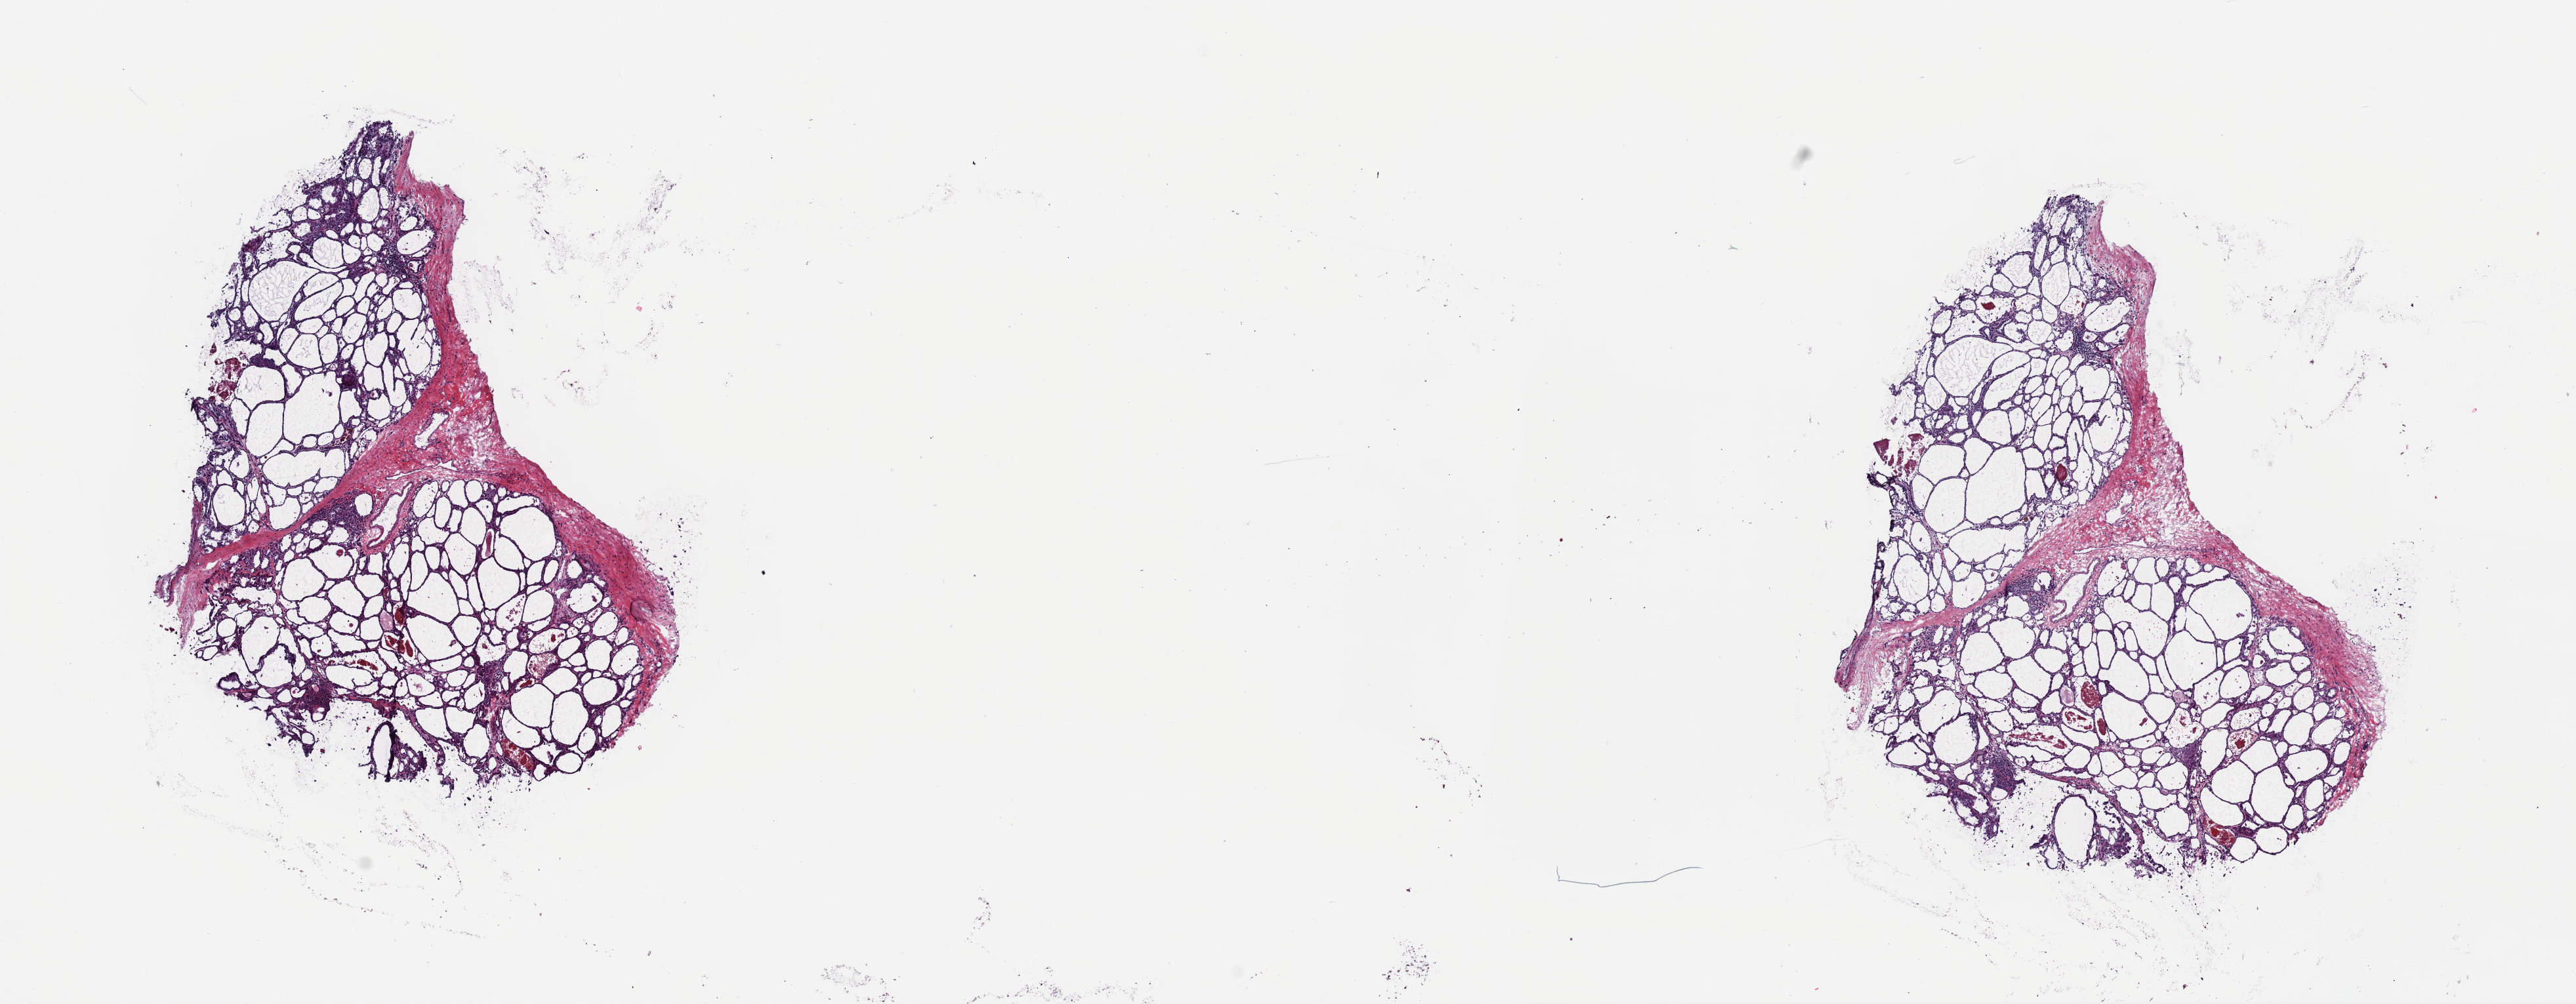
Hematoxylin and eosin (H&E) stained whole-slide image, shown as a low-resolution overview of the whole scanned area (about 15.5 x 6.0 mm, from a 40x scan); frozen section from the top of the tissue portion; thyroid, primary tumour sample. Patient: female, age at initial diagnosis 63 years. Composition of this section per pathologist review: tumour cells 70%, tumour nuclei 95%, normal cells 0%, stromal cells 30%, necrosis 0%. Inflammatory infiltration, as recorded: lymphocyte infiltration 10%, monocyte infiltration 0%, neutrophil infiltration 0%.
Laterality: left. Histologic diagnosis: Papillary carcinoma, follicular variant (thyroid gland). AJCC pathologic stage: I (7th edition).